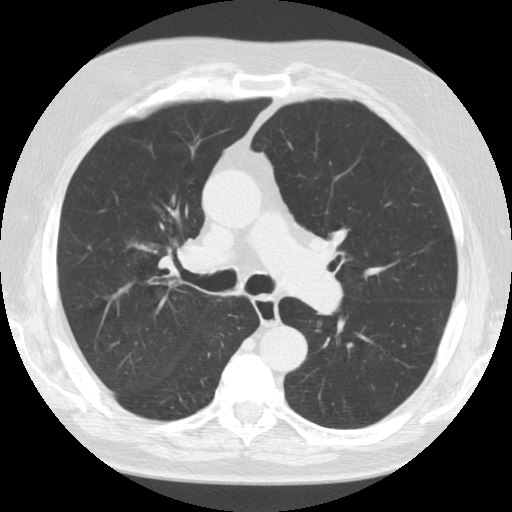
Axial slice from a low-dose chest CT screening exam, baseline annual screen, lung window (W 1500 / L -600 HU), 2.5 mm slice thickness, standard (soft-tissue) reconstruction kernel (STANDARD), slice 48 of 125 in the series. Male participant, aged 72 years at enrolment. Former smoker at enrolment.
- Expert-annotated lung lesion, bounding box [x1, y1, x2, y2] px = [140, 215, 220, 299].
- Screening reader's record for this exam: no non-calcified nodule ≥4 mm recorded.
- Lung cancer was diagnosed 779 days after this screen: small cell carcinoma, NOS, right upper lobe, stage IV (AJCC 6th edition), 7 mm at pathology.